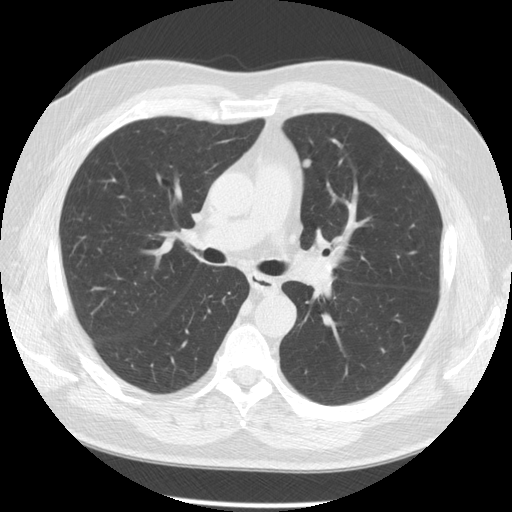
Chest CT (low-dose screening protocol), one axial image; second screening round (one year after baseline); lung window (W 1500 / L -600 HU); standard (soft-tissue) reconstruction kernel (STANDARD); slice 53 of 137 in the series. Male, age 64 years at enrolment. Former smoker at enrolment.
• Expert reader's lesion annotation, bounding box (x1, y1, x2, y2) in pixels: (288, 143, 334, 178).
• The screening reader recorded 2 non-calcified nodules or masses ≥4 mm on this exam (left upper lobe, left lower lobe); which of them this box marks is not recorded.
• Official screen result: positive, other.
• Lung cancer was diagnosed 58 days after this screen: squamous cell carcinoma, NOS, left upper lobe, poorly differentiated (G3), stage IA (AJCC 6th edition), 14 mm at pathology.